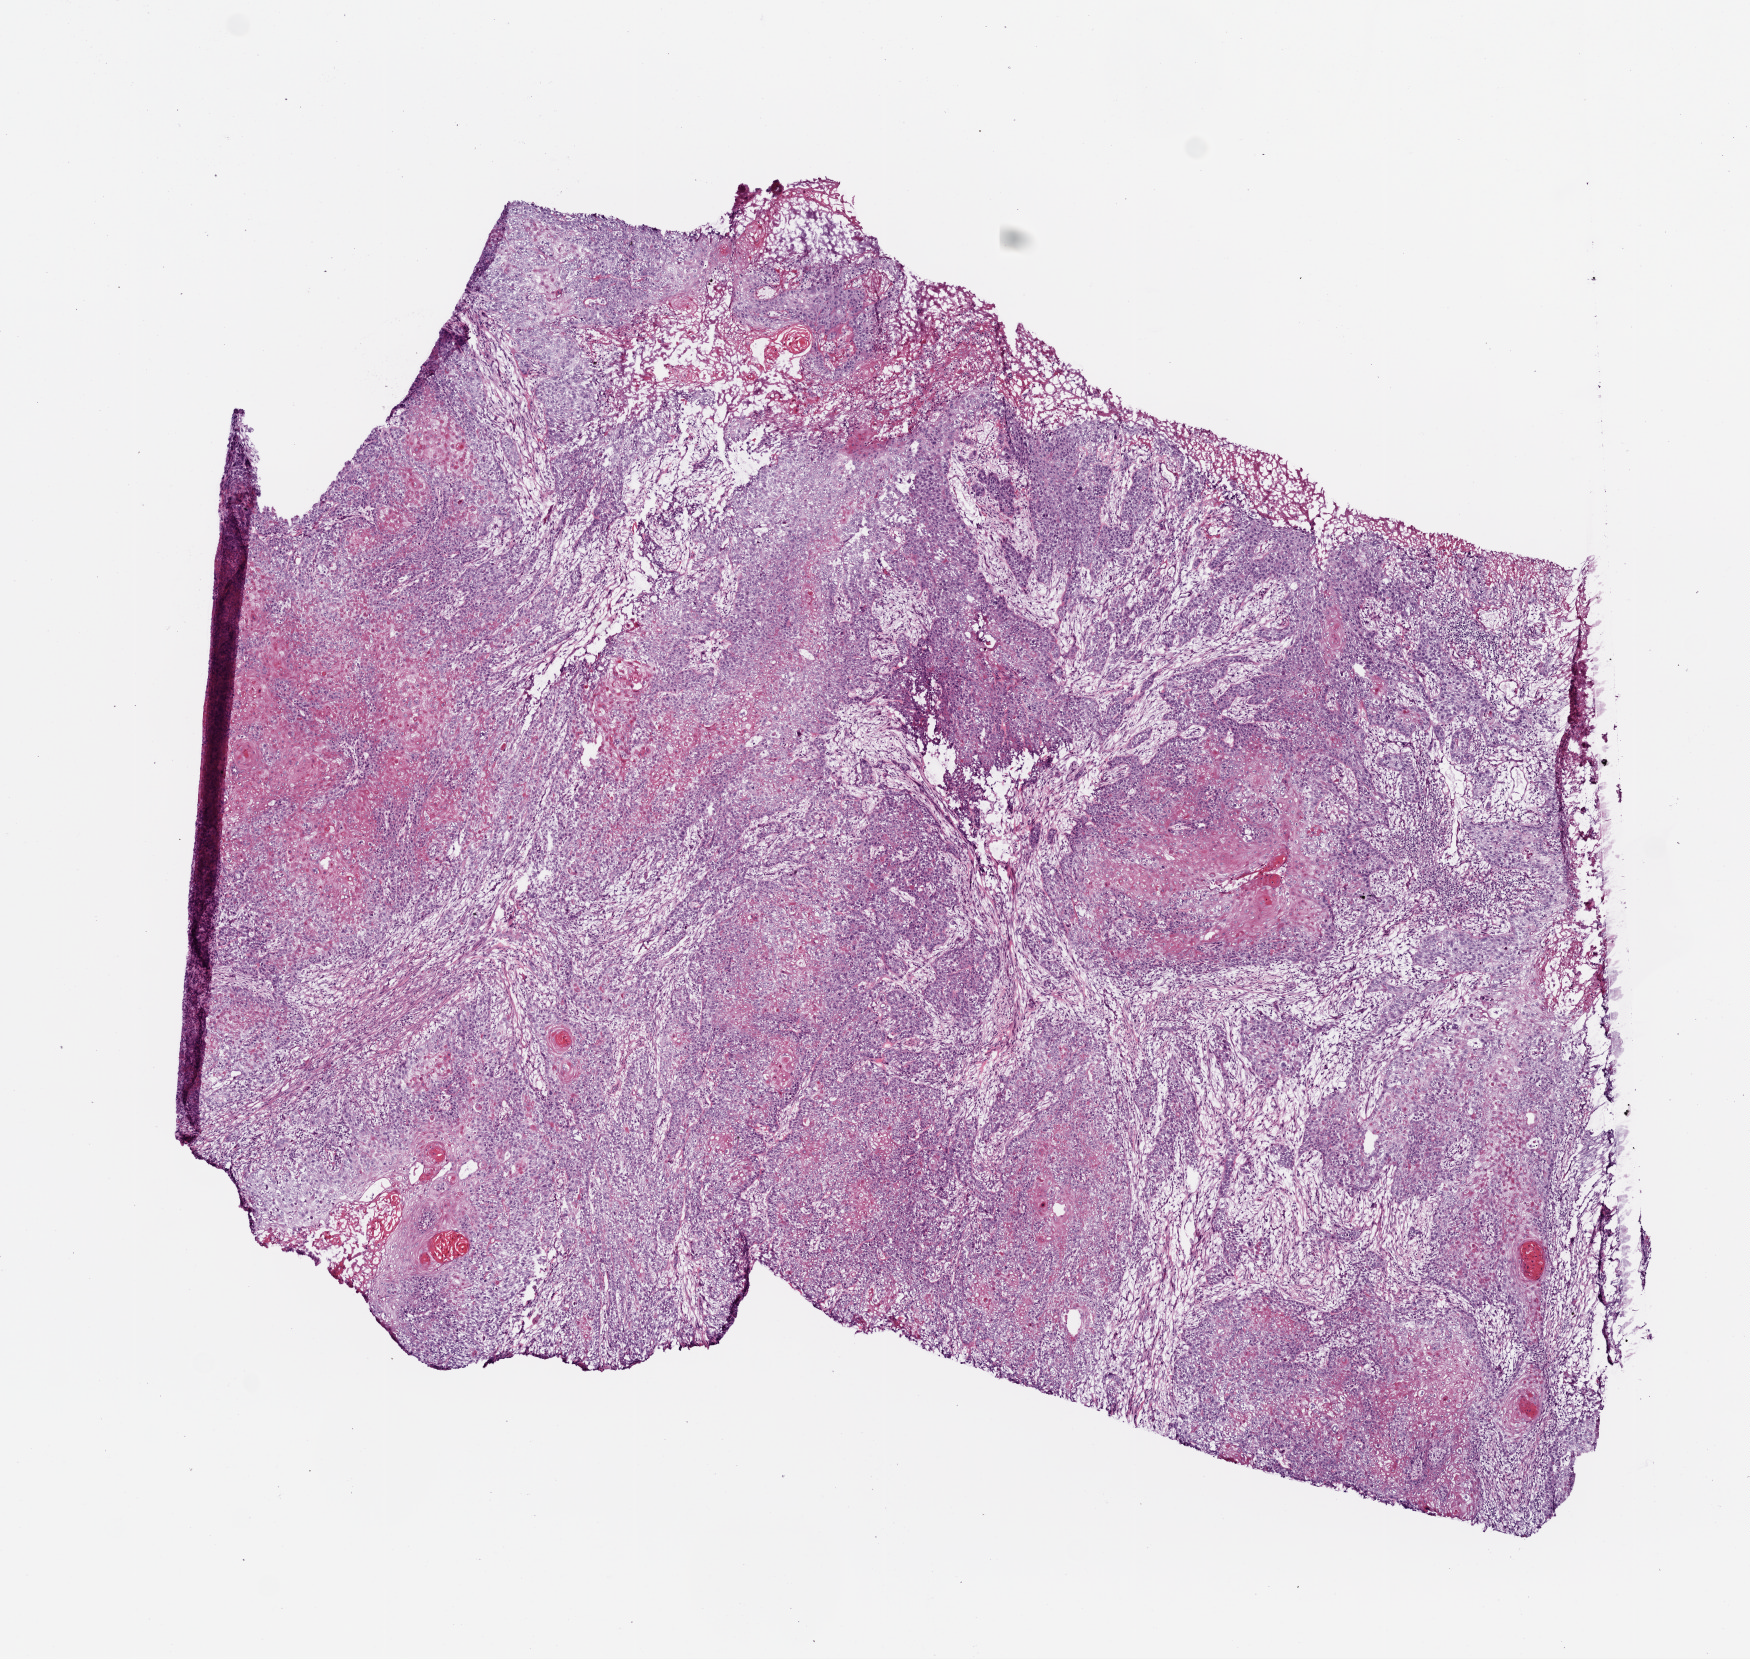
H&E whole-slide image, whole scanned area (about 7.0 x 6.7 mm, from a 20x scan) shown as a low-resolution overview, frozen section from the top of the tissue portion, sample: primary tumour, head and neck. Female patient; age at initial diagnosis 46 years. Histologic grade: G2 (moderately differentiated). Slide review estimates, as recorded: tumour cells 99%, tumour nuclei 80%, normal cells 0%, stromal cells 0%, necrosis 1%. Inflammatory infiltration, as recorded: lymphocyte infiltration 10%, neutrophil infiltration 1%.
- AJCC pathologic stage: II
- pathologic diagnosis: Squamous cell carcinoma, NOS (tongue, NOS)
- laterality: left
- TNM: T2 N0